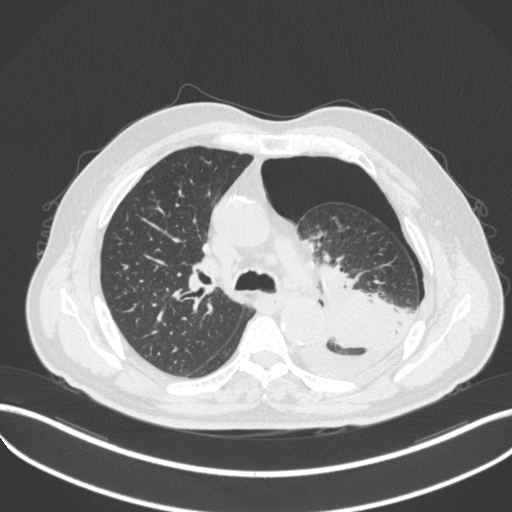
Chest CT, one axial slice. Slice 338 of 466 in the series (ordered by position). Reconstruction kernel B31f. 120 kVp. Lung window (W 1500 / L -600 HU). 512 × 512 image matrix, field of view 400 × 400 mm. Patient: male, 76 years. From the clinical record (not read from this slice): clinical TNM (as recorded): T3 N0 M1b.
Outlined on this slice (rectangle marked by the reading radiologist):
- lung tumour (recorded histology: adenocarcinoma): bounding box (x1, y1, x2, y2) in pixels: (292, 290, 396, 372)